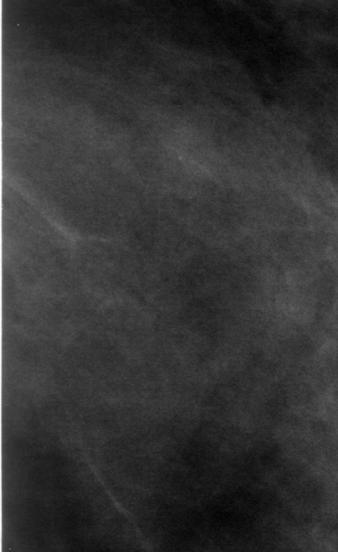
Crop from a digitized film mammogram around one marked abnormality, left breast, CC view.
- Finding: mass, shape round, margins ill defined; BI-RADS assessment category 4; pathology (as recorded): benign.